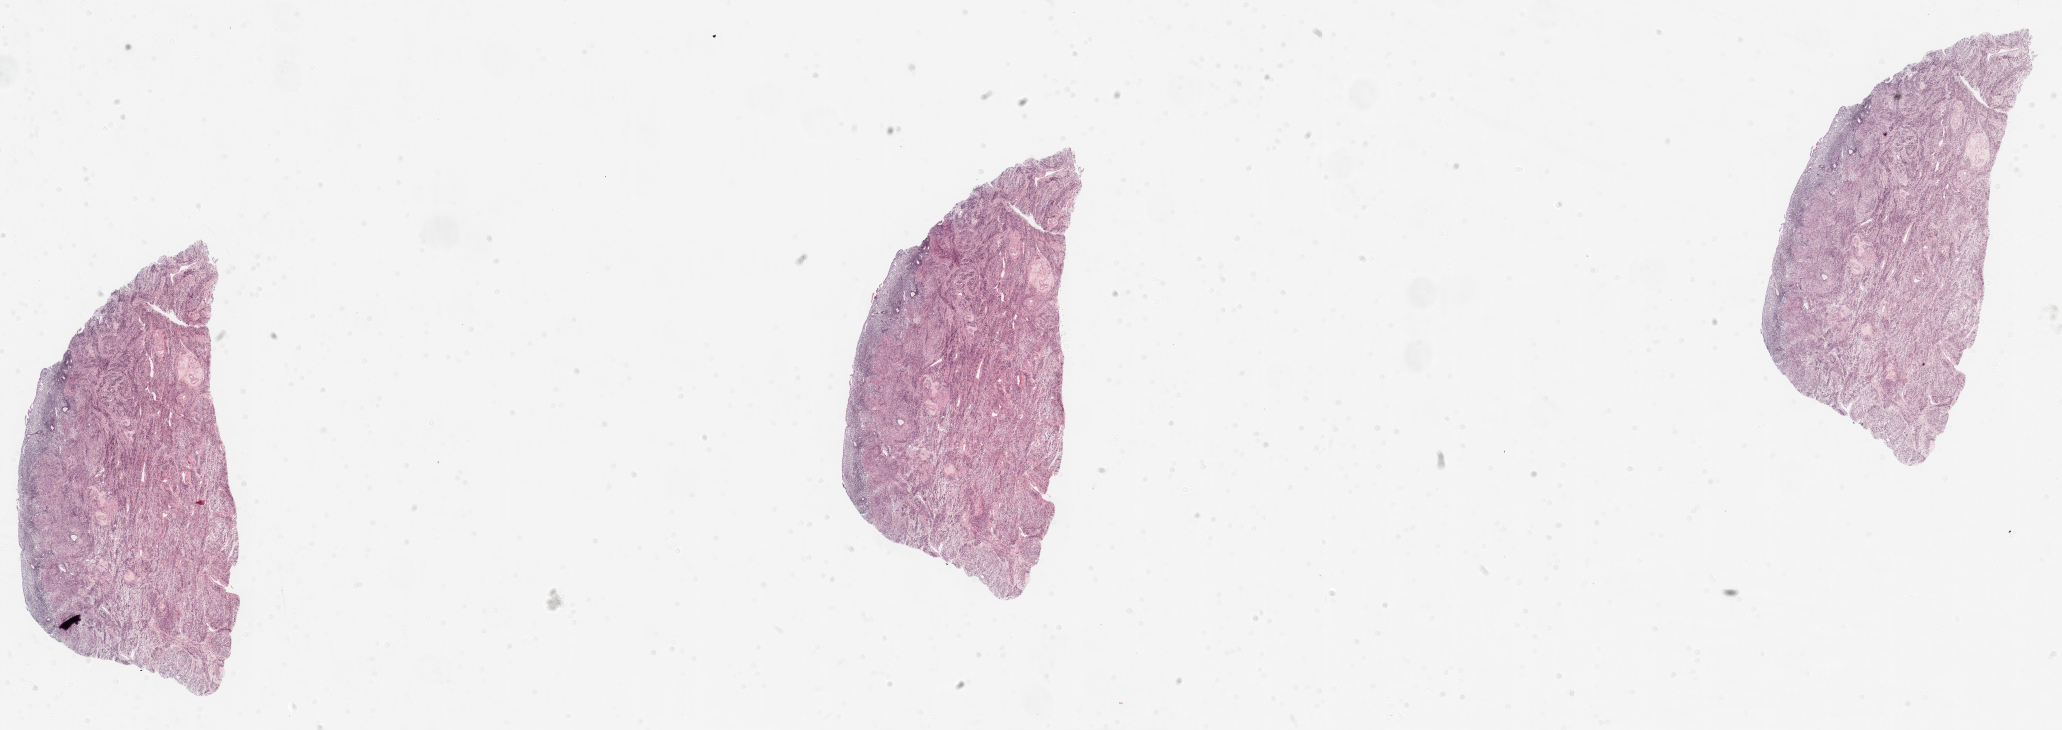
Whole-slide histology image, Hematoxylin and eosin (H&E) stained, whole scanned area (about 33.1 x 11.7 mm, acquisition: 20x scan) shown as a low-resolution overview; frozen section from the top of the tissue portion; solid tissue normal (non-tumour tissue) sample from the ovary. Patient: female, age at initial diagnosis 62 years.
This section: solid tissue normal sample (biorepository sample class). Patient diagnosis: Serous cystadenocarcinoma, NOS.